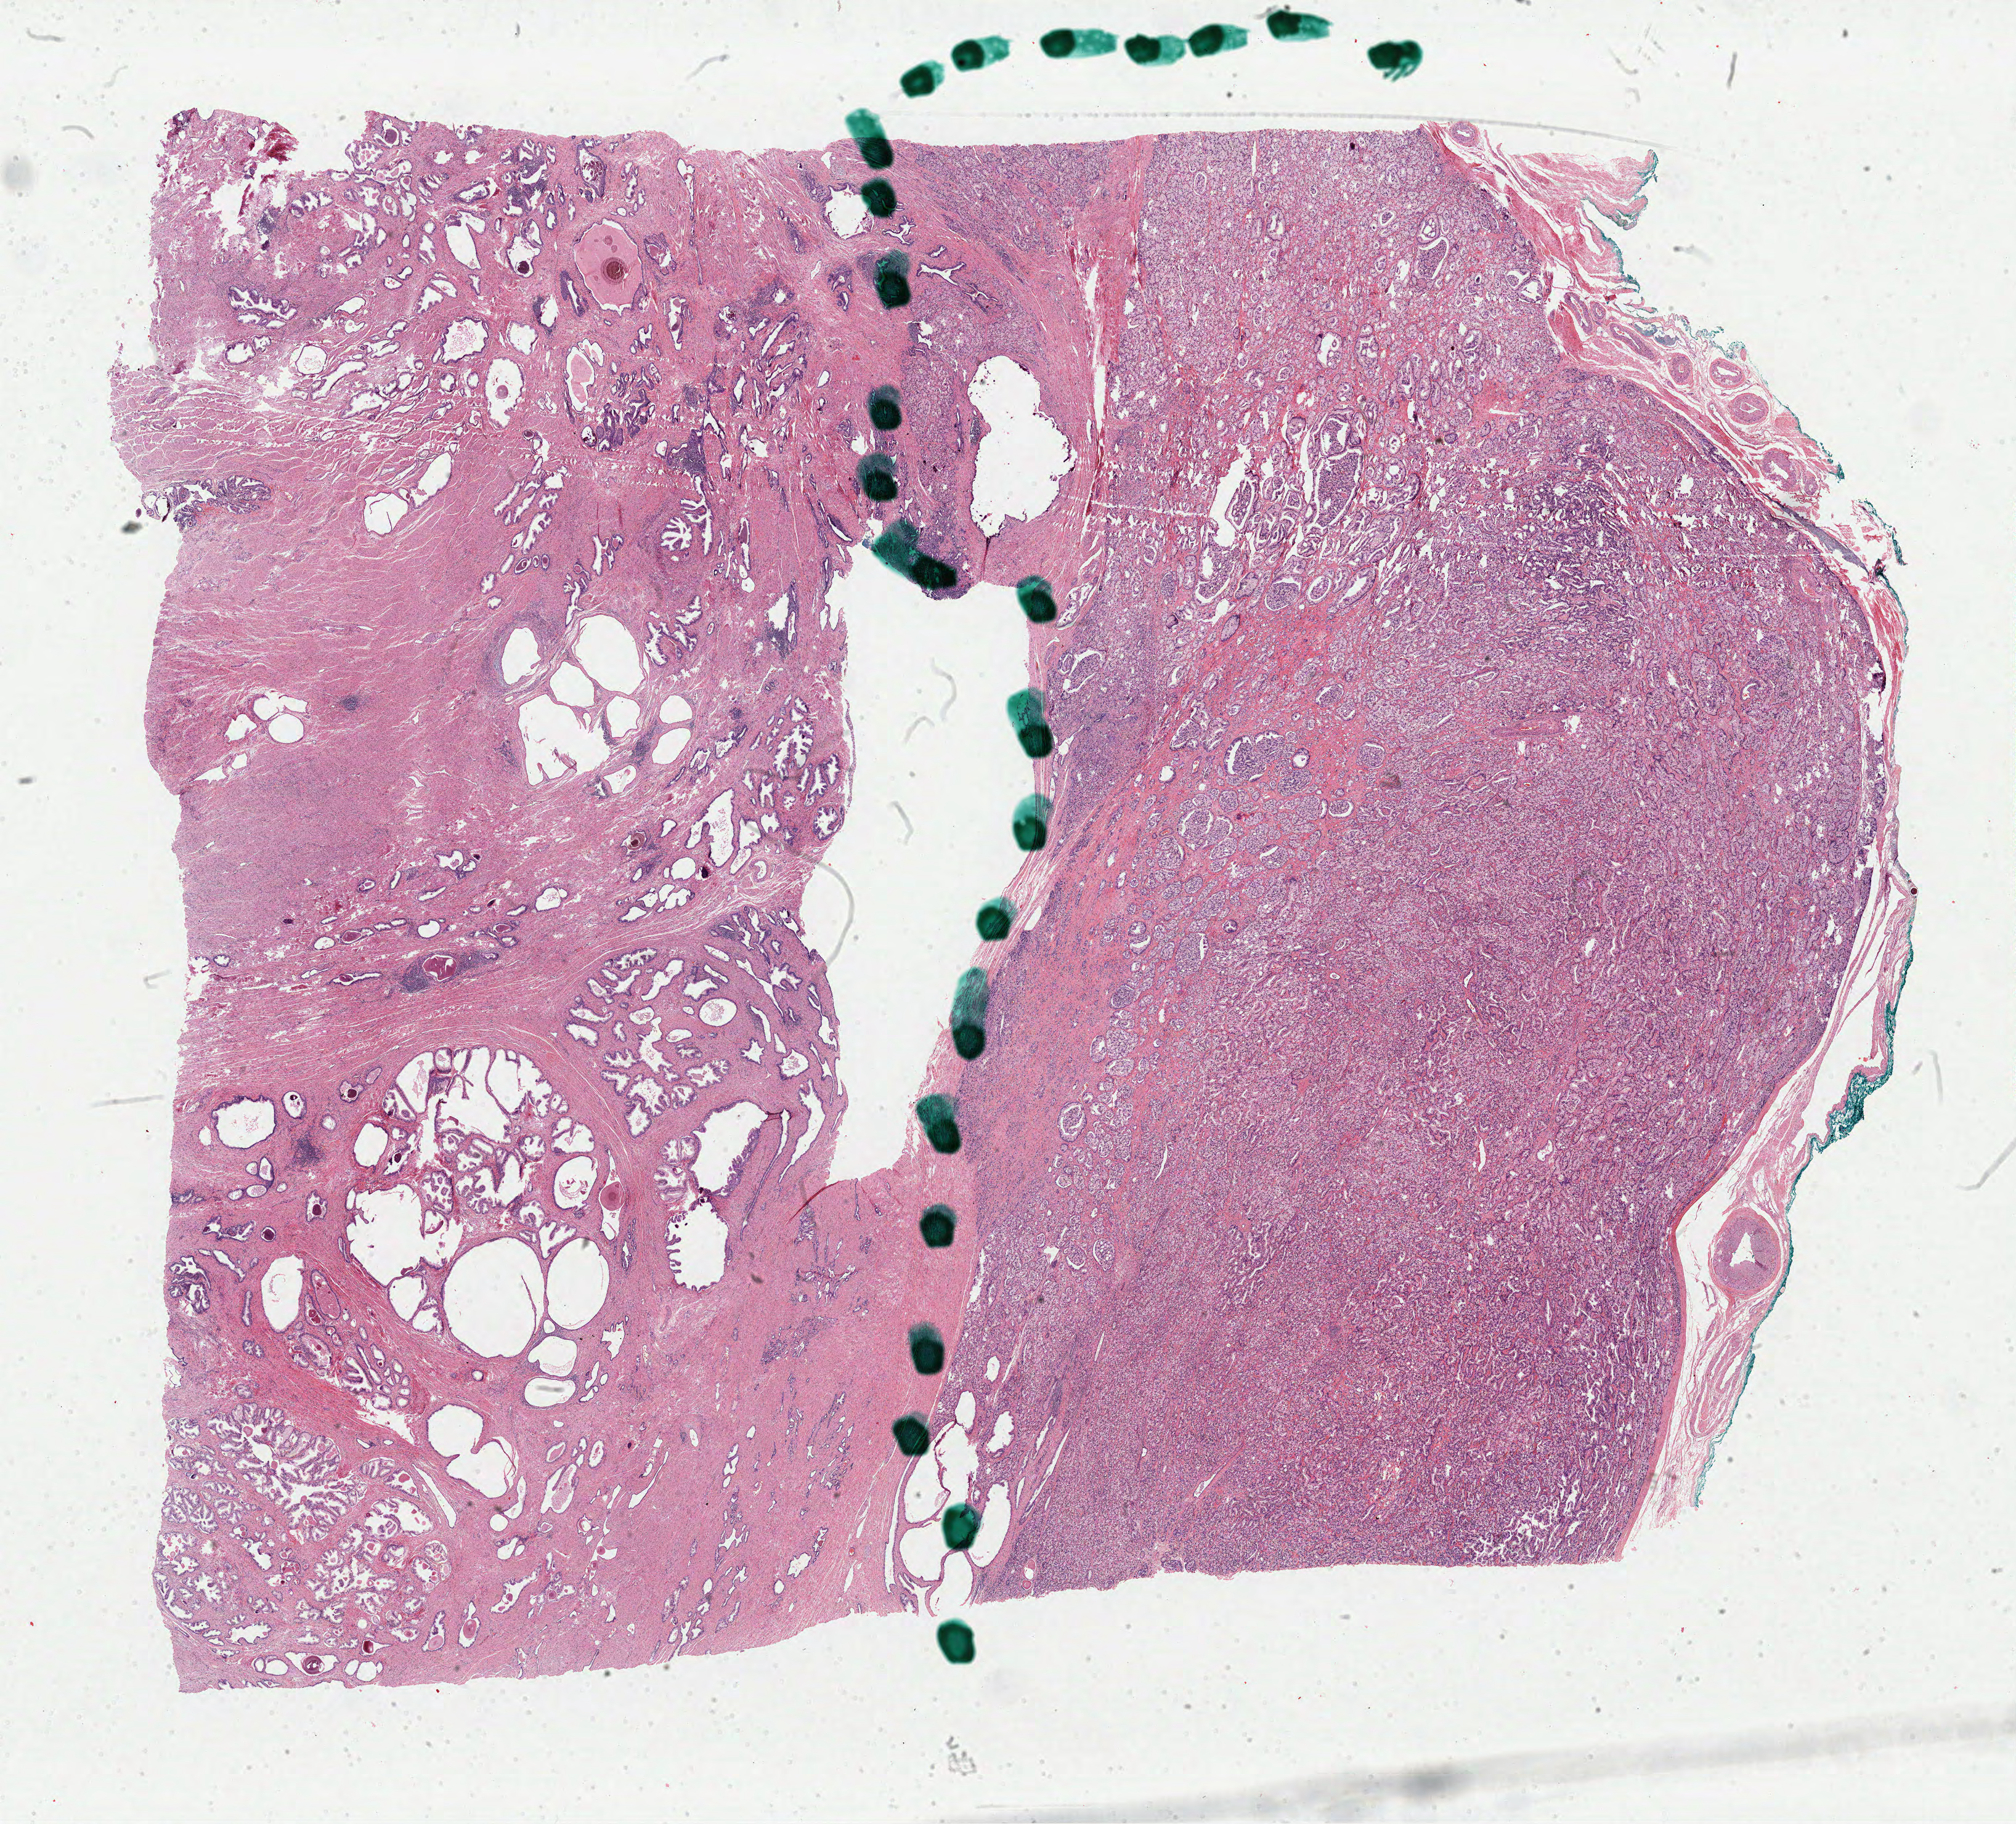
Whole-slide histology image, H&E — whole scanned area (about 25.8 x 23.4 mm) shown as a low-resolution overview. FFPE section. Prostate, primary tumour sample. Male, age 68 years at initial diagnosis. Gleason score: 9 (4+5).
- diagnosis: Adenocarcinoma, NOS
- lymph nodes positive (case pathology): 0 of 14 examined